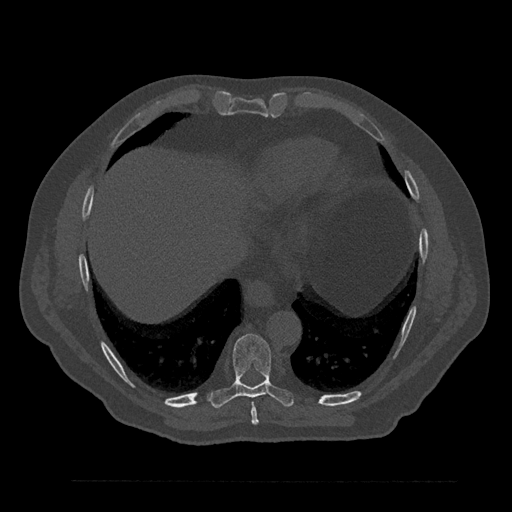
CT including the spine, one axial slice. Slice 410 of 797 in the series (ordered by position). 120 kVp. Bone window (W 1800 / L 400 HU). 0.5 mm slice thickness. 512 × 512 image matrix, field of view 430 × 430 mm. Patient: male, 61 years. From the clinical record (not read from this slice): primary cancer: prostate.
Annotated regions visible in this slice (semi-automatically segmented with operator editing):
- T8 vertebra: bounding box [x1, y1, x2, y2] px = [251, 402, 259, 425]
- T9 vertebra: [209, 334, 295, 408]